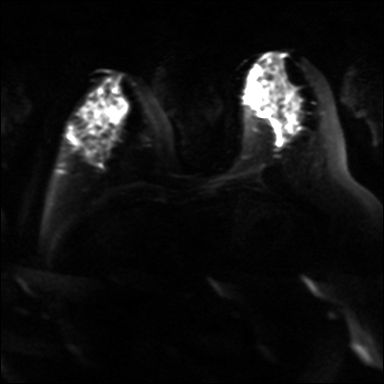
Breast MRI, one axial slice; position 12 of 36 along the scan axis; diffusion-weighted series; image 2 of 4 stored at this slice position (different b-values; order by instance number); 3 T; 4 mm slice thickness; 384 × 384 image matrix, field of view 320 × 320 mm. Female patient.
Annotated regions visible in this slice (manually delineated by an expert):
- tumour on diffusion-weighted imaging: bounding box [x1, y1, x2, y2] px = [275, 119, 281, 124]